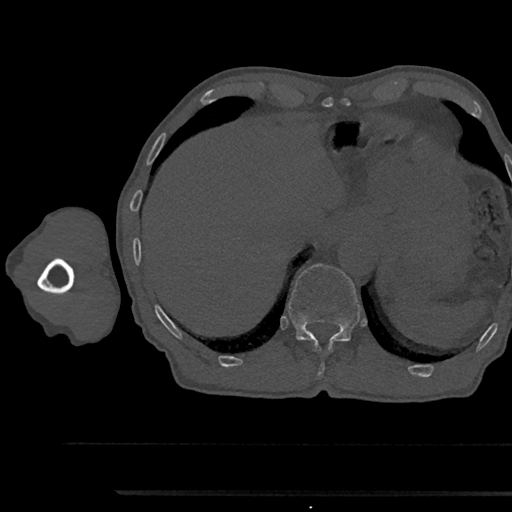
CT including the spine, one axial slice. Position 744 of 797 along the scan axis. Reconstruction kernel Br40s/3. 120 kVp. Bone window (W 1800 / L 400 HU). 0.5 mm slice thickness. 512 × 512 image matrix, field of view 367 × 367 mm. Patient: male, 79 years. Case-level facts recorded for this patient, not image findings: primary cancer: prostate.
Outlined on this slice (semi-automatically segmented with operator editing):
- T11 vertebra: bounding box [x1, y1, x2, y2] px = [315, 344, 332, 374]
- T12 vertebra: [288, 264, 360, 345]